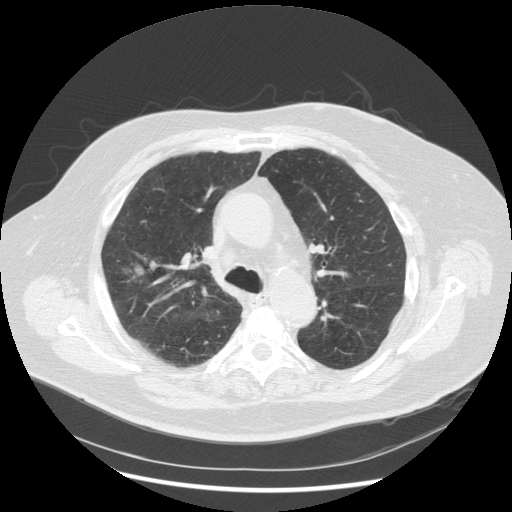
Low-dose screening chest CT, one axial slice. Position 187 of 263 along the scan axis. 120 kVp. Lung window (W 1500 / L -600 HU). 512 × 512 image matrix, field of view 400 × 400 mm.
Structures marked on this image (outlined manually by an expert reader):
- lesion 1 (tumor, upper lobe of right lung): bounding box (x1, y1, x2, y2) in pixels: (127, 266, 144, 282)